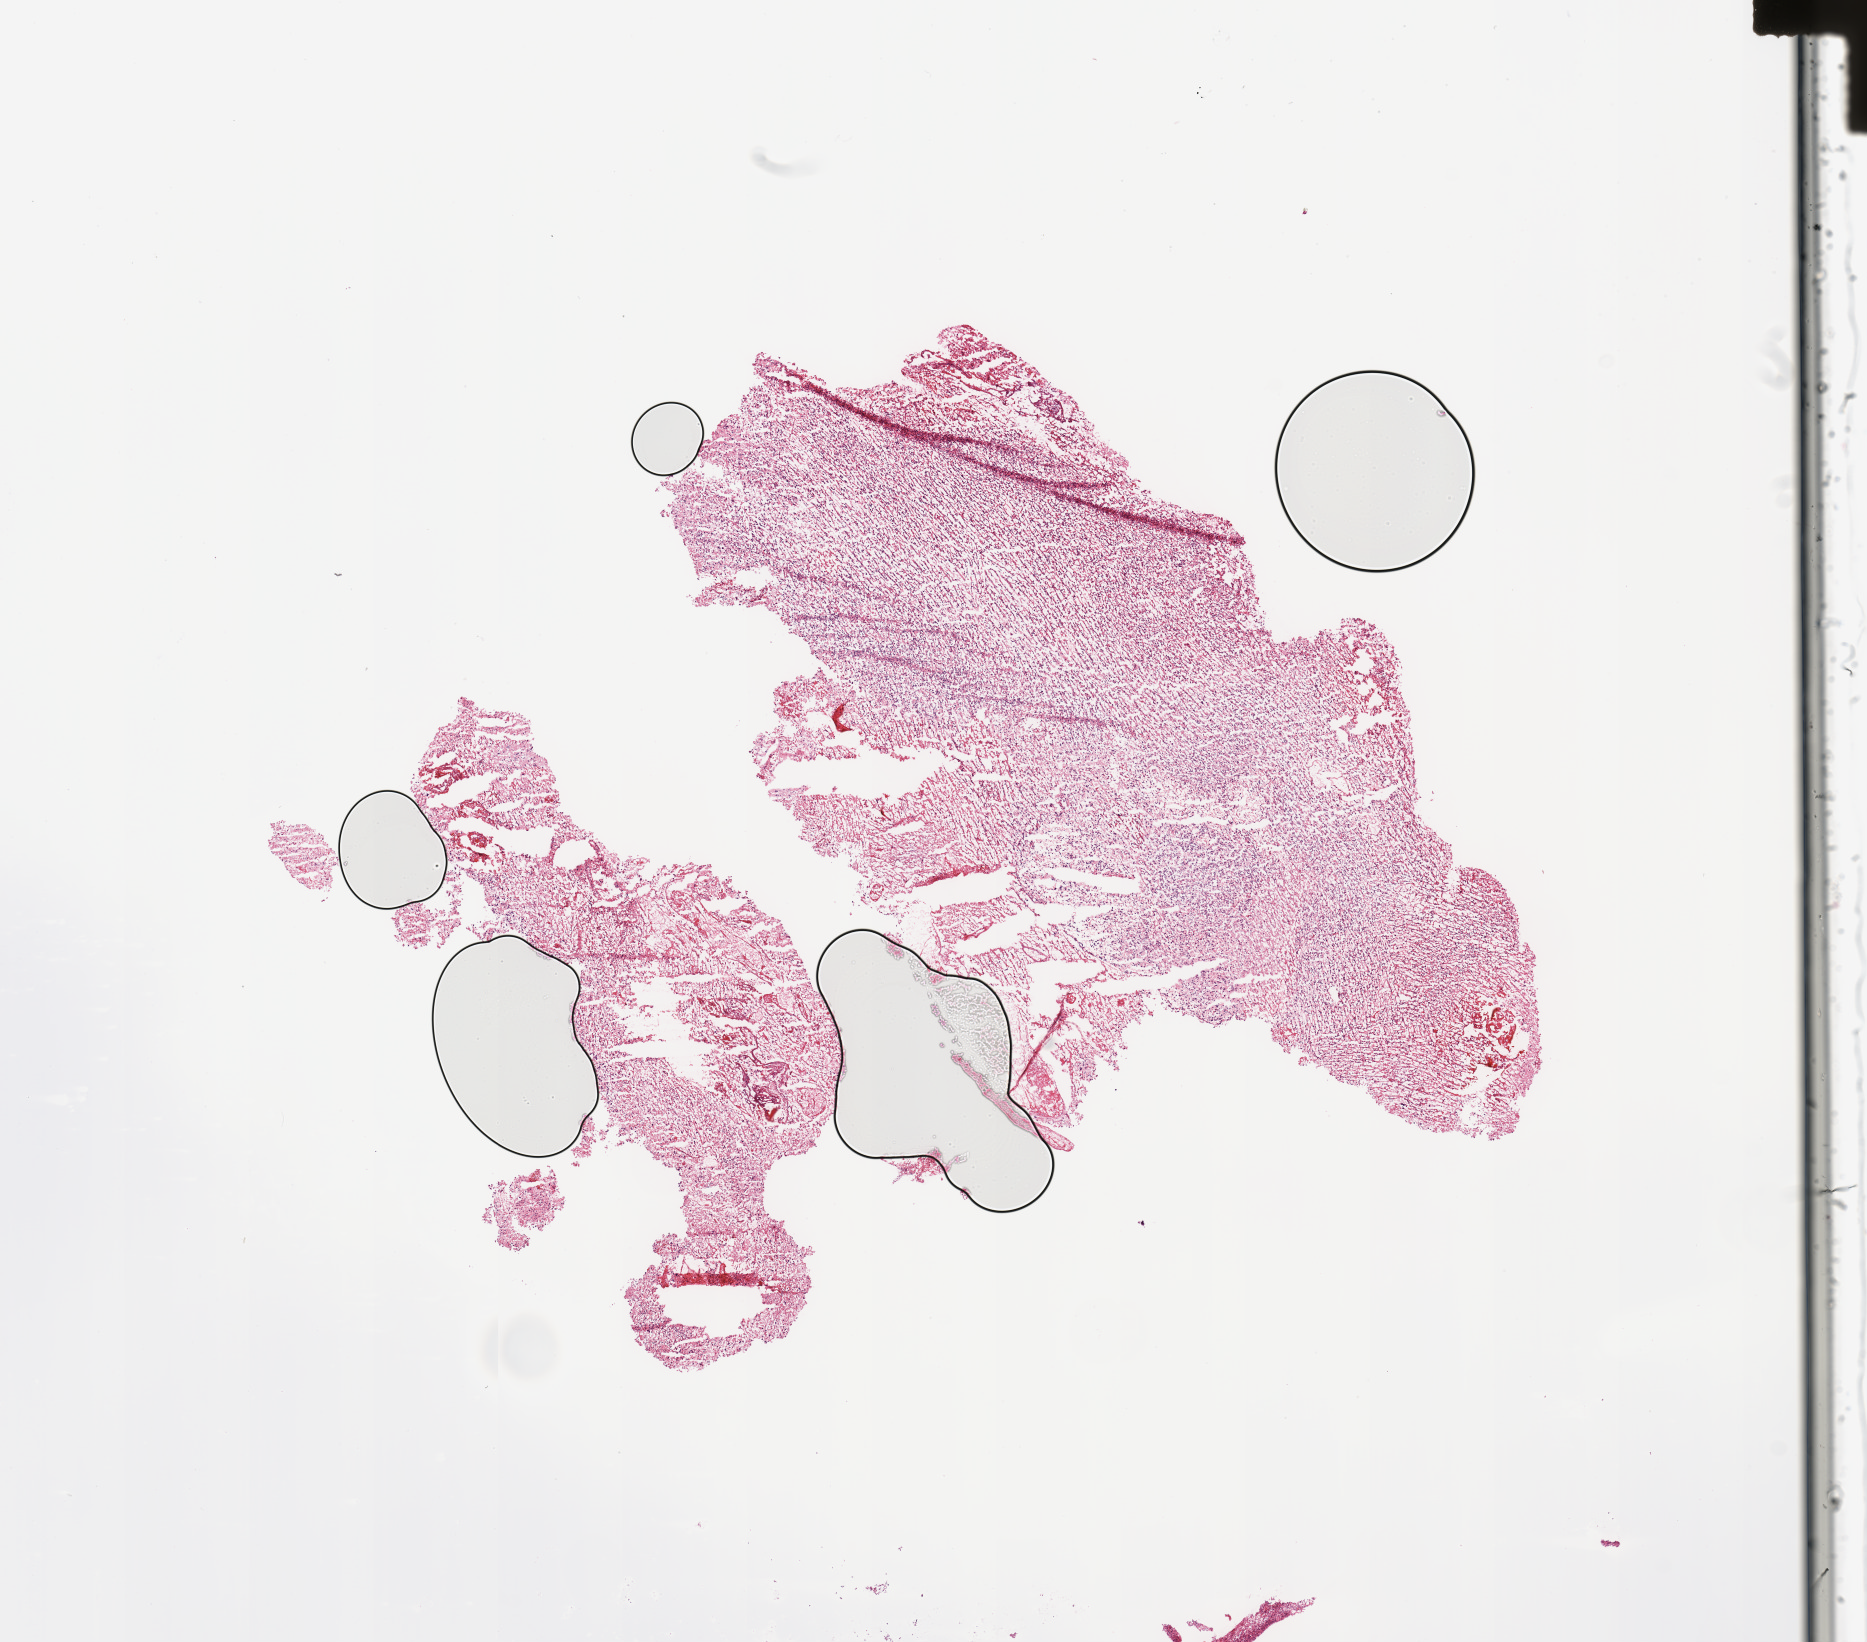
Whole-slide histology image, H&E-stained, whole scanned area (about 14.8 x 13.0 mm, slide scanned at 20x) shown as a low-resolution overview; brain, tissue type not recorded.
Patient diagnosis (cohort enrolment): glioblastoma multiforme (brain).